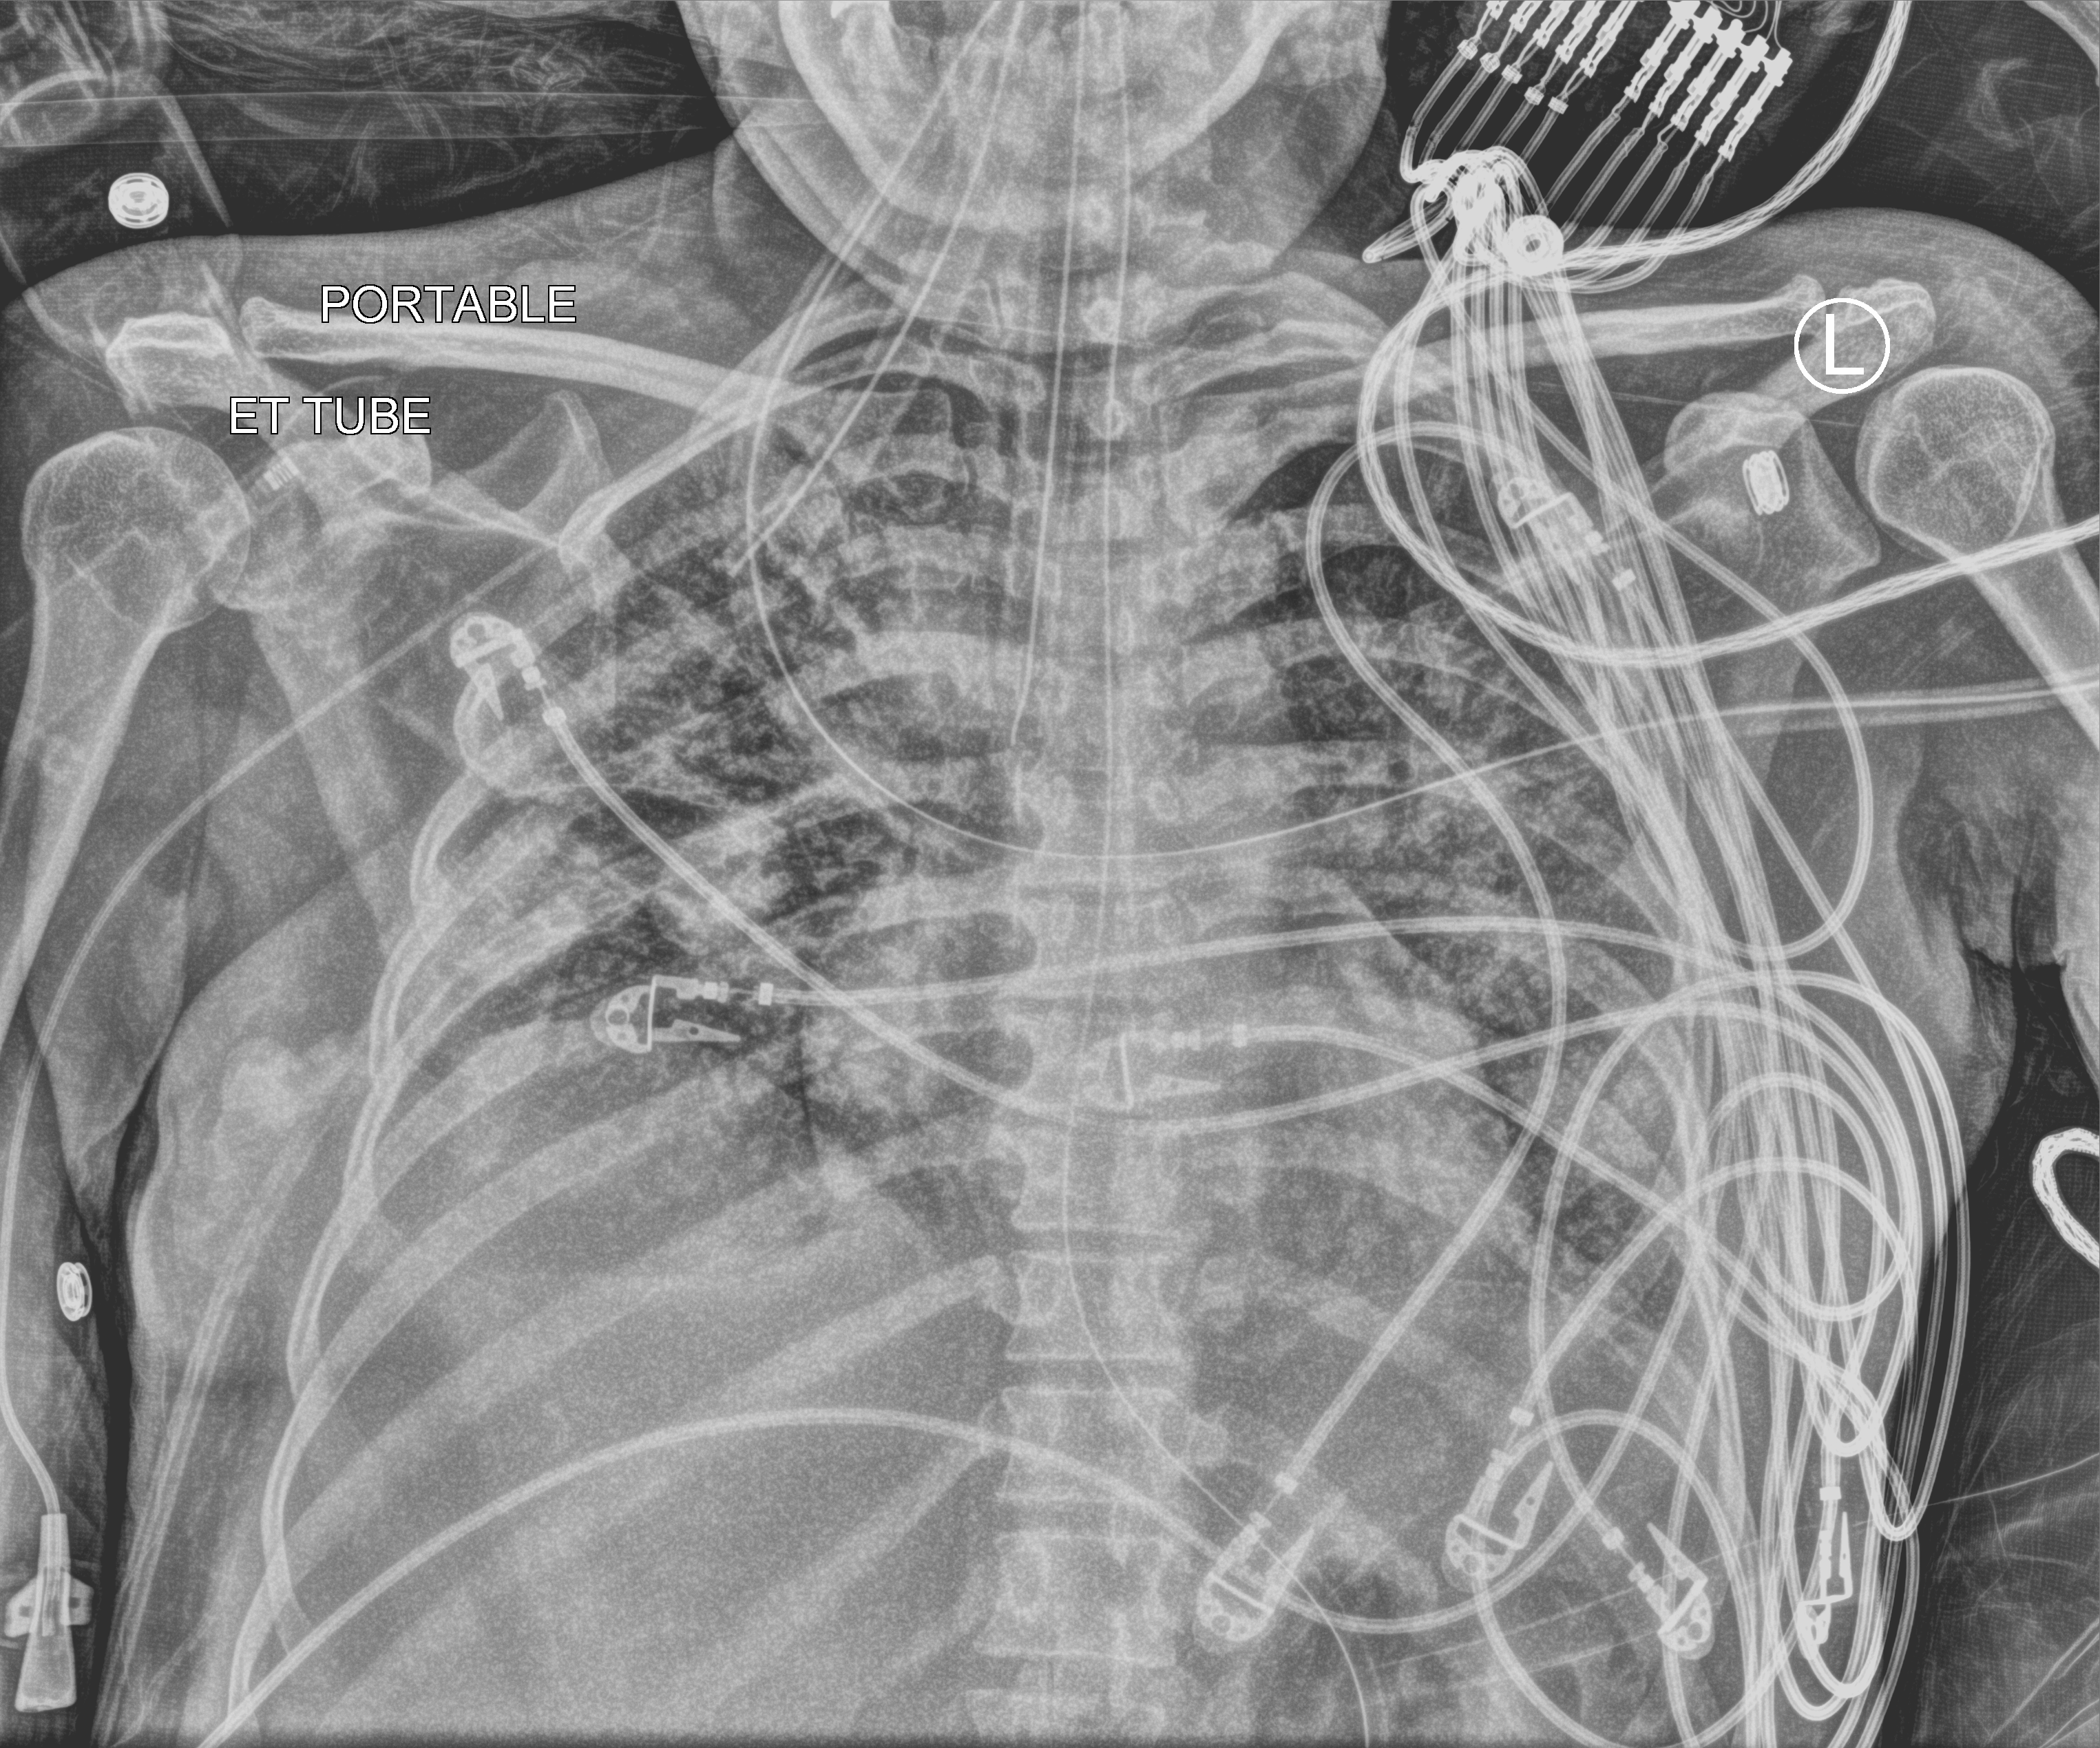
Bedside chest radiograph (computed radiography); anteroposterior (AP) projection. Female patient hospitalised with COVID-19, age 18–59 years.
Hospital-stay facts (about this admission, not read from this image; timing relative to this image not recorded): mechanically ventilated during this hospital stay: yes.